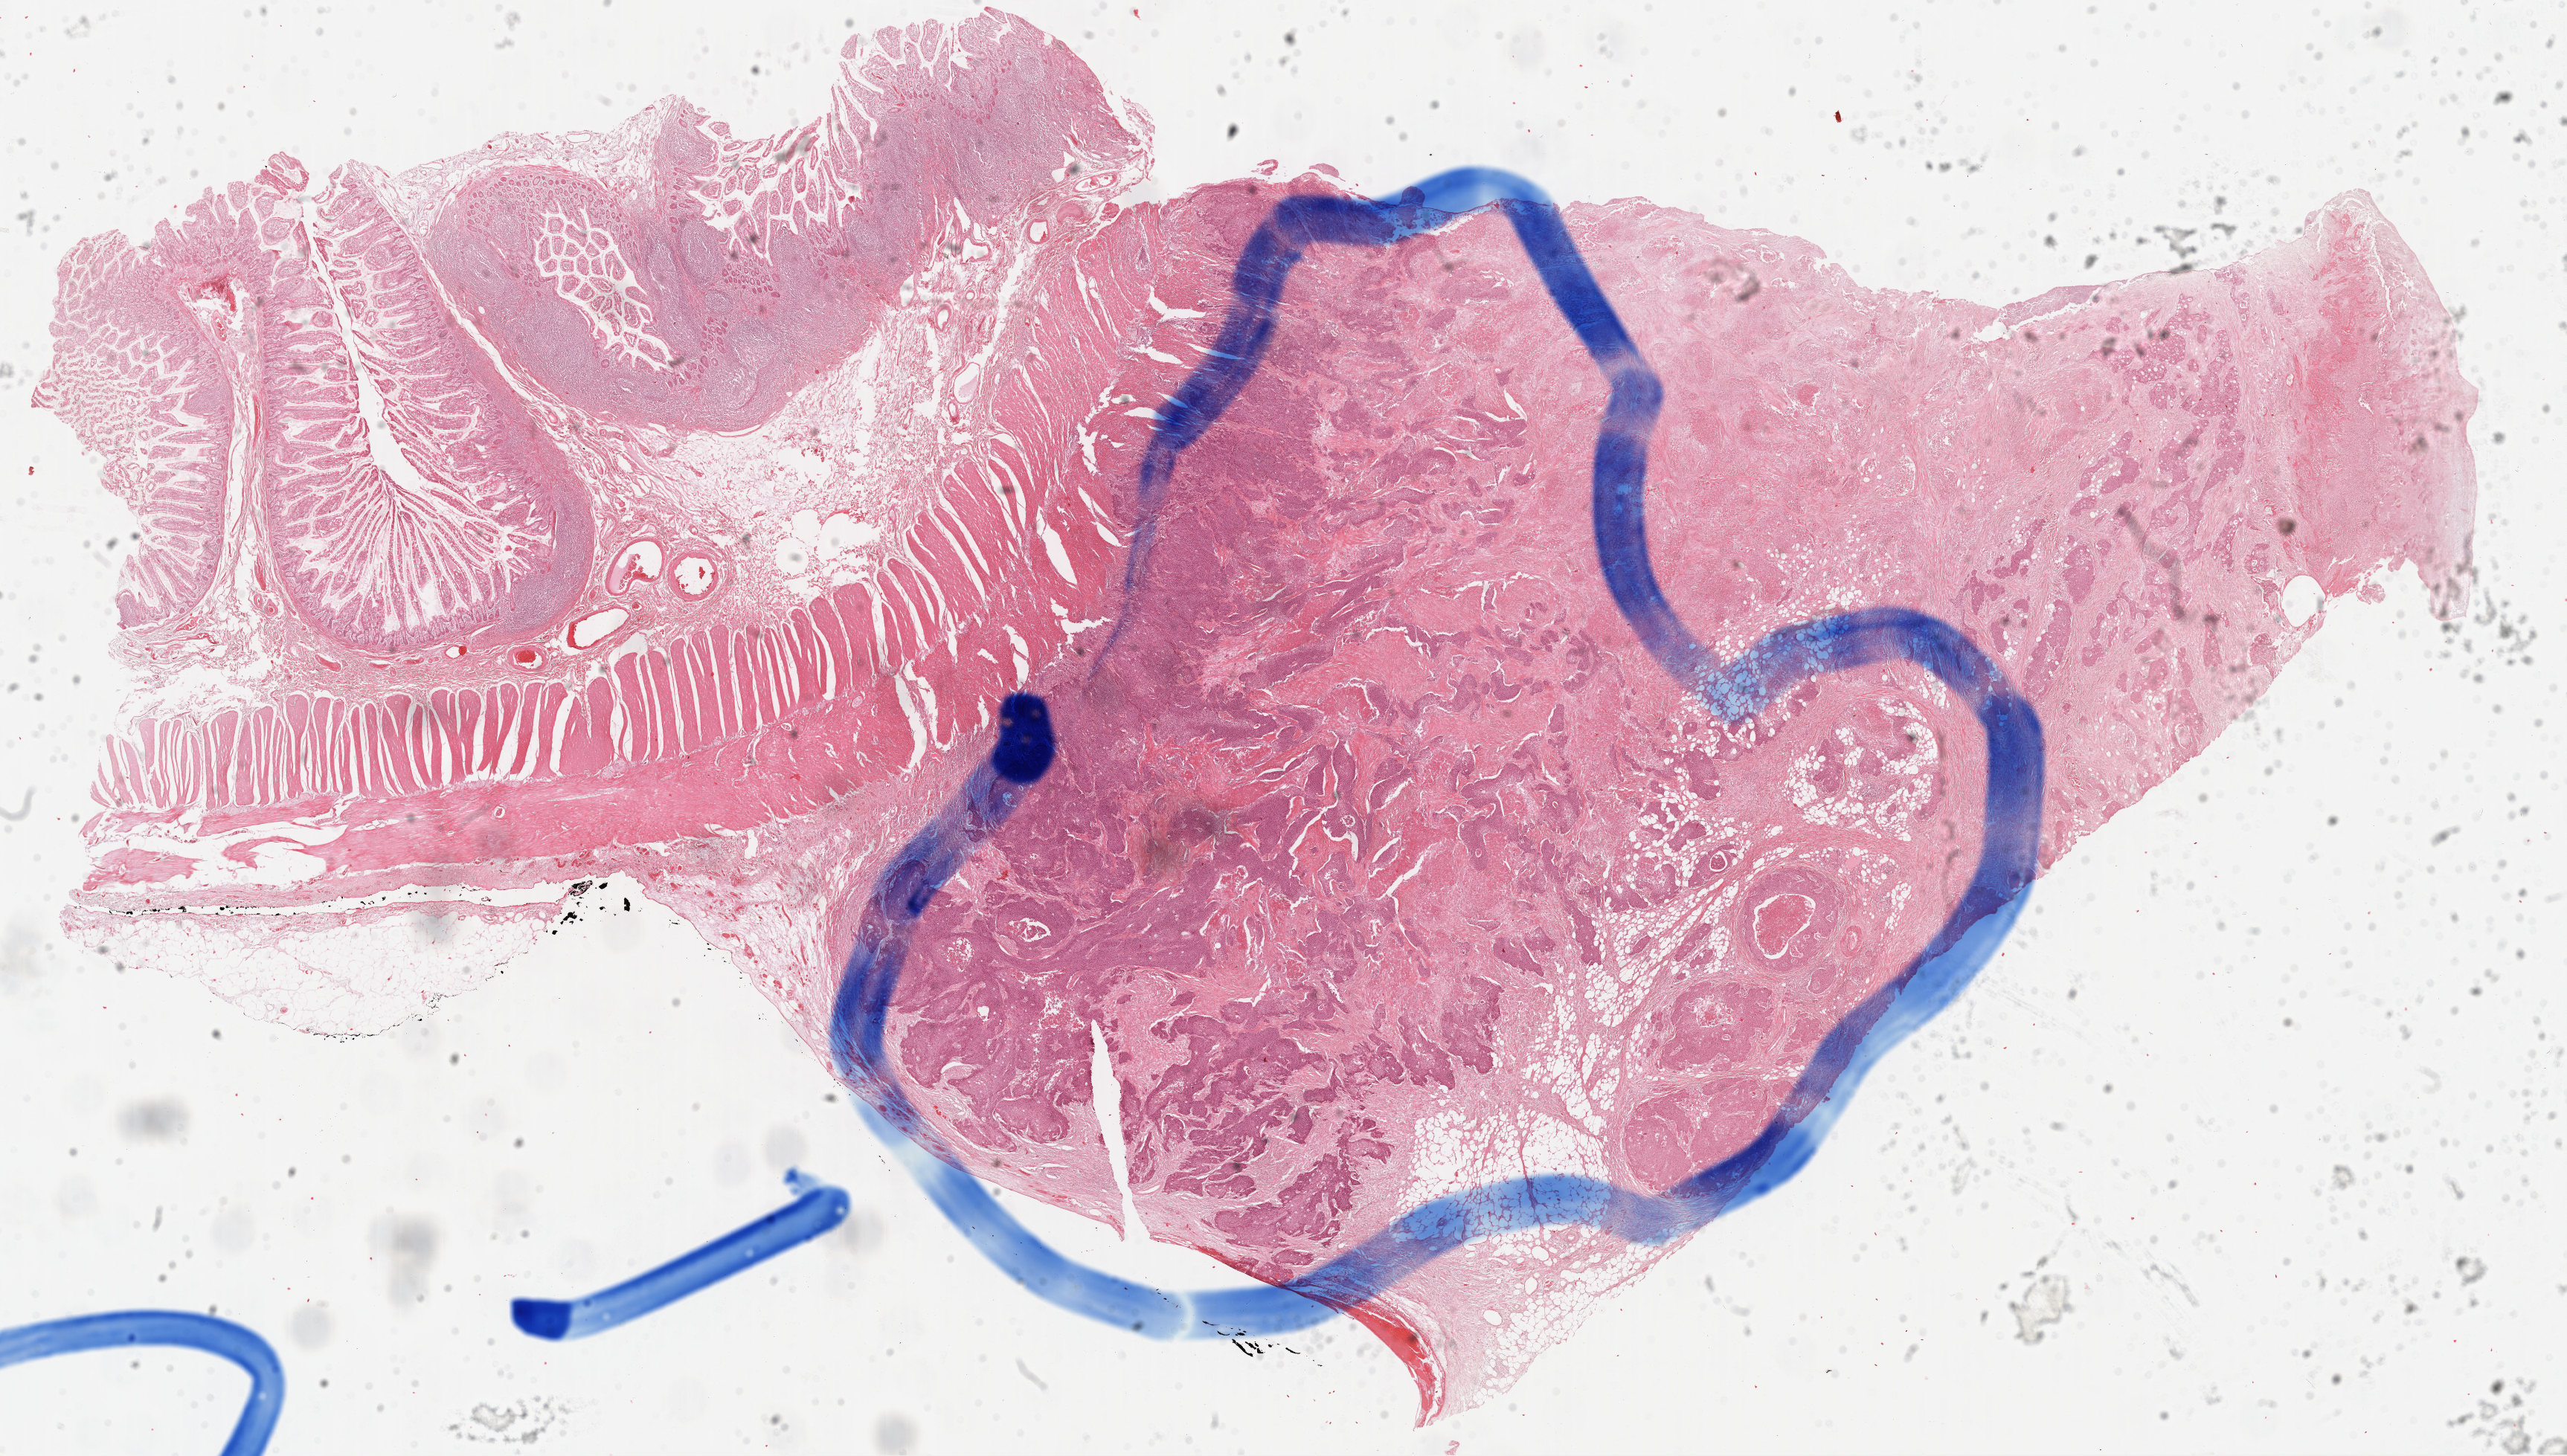
Whole-slide histology image, H&E-stained, shown as a low-resolution overview of the whole scanned area (about 27.3 x 15.5 mm, slide scanned at 40x). FFPE section. Sample: primary tumour, colon. Male, age 50 years at initial diagnosis.
Lymph nodes positive (case pathology): 8 of 12 examined. AJCC pathologic stage: IIIC. Pathologic diagnosis: Adenocarcinoma, NOS (cecum).